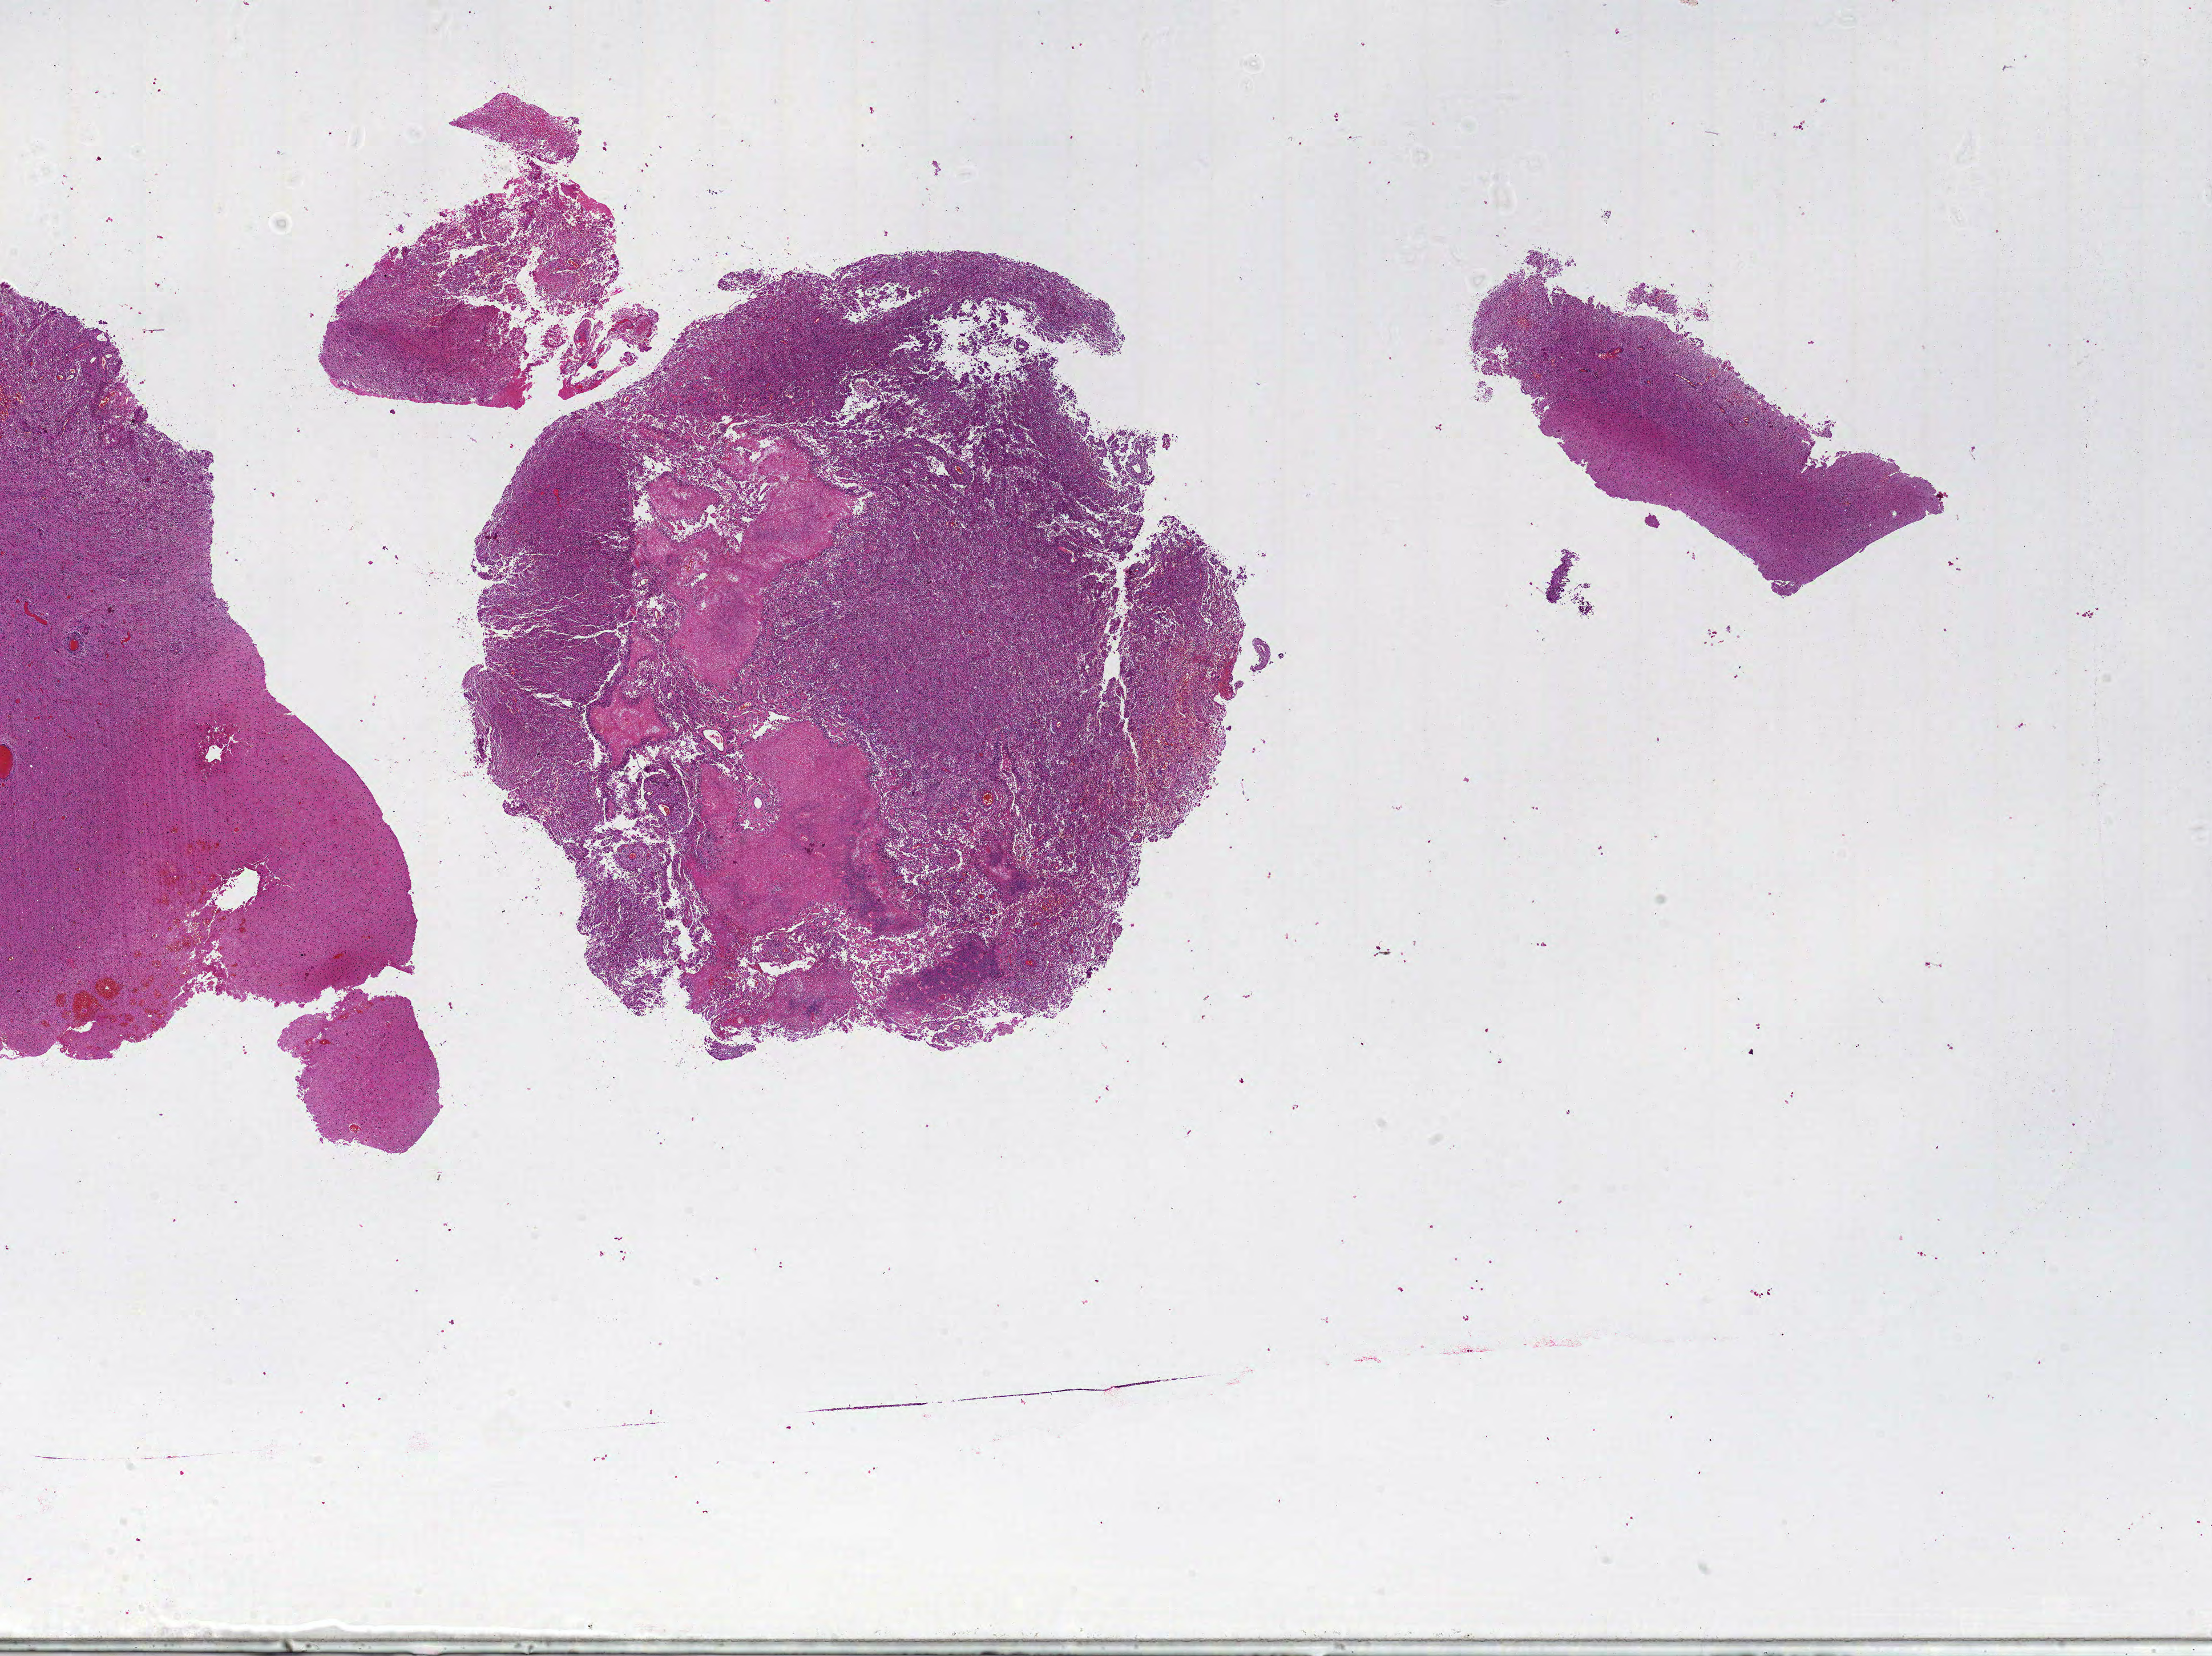
Whole-slide histology image, H&E — shown as a low-resolution overview of the whole scanned area (about 31.0 x 23.2 mm, slide scanned at 20x); formalin-fixed paraffin-embedded (FFPE) diagnostic section; brain, primary tumour sample. Male, age 46 years at initial diagnosis.
Diagnosis: Glioblastoma.